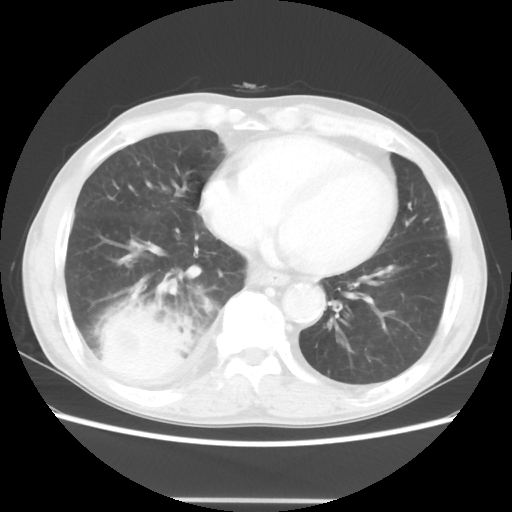
Chest CT, one axial slice; position 14 of 48 along the scan axis; lung window (W 1500 / L -600 HU); 5 mm slice thickness; 512 × 512 image matrix. Patient: male, 66 years. From the clinical record (not read from this slice): clinical TNM (as recorded): T4 N1 M1.
Annotated regions visible in this slice (bounding box drawn by a radiologist):
- lung tumour (recorded histology: small cell carcinoma): bounding box [x1, y1, x2, y2] px = [92, 295, 194, 394]